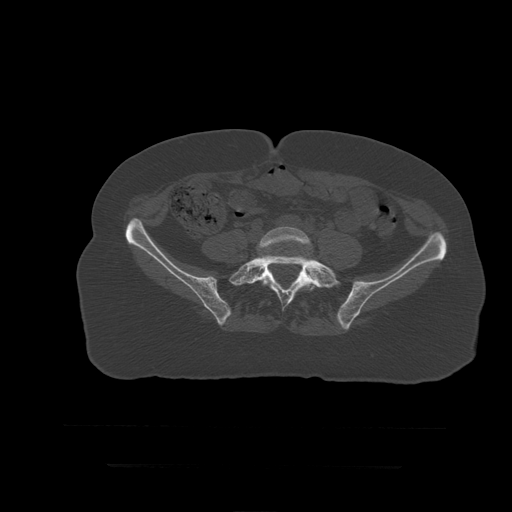
CT including the spine, one axial slice; slice 59 of 399 in the series (ordered by position); bone window (W 1800 / L 400 HU); 1.25 mm slice thickness; 512 × 512 image matrix. Patient age 41 years. From the clinical record (not read from this slice): primary cancer: breast.
Structures marked on this image (semi-automatic segmentation, software-assisted and operator-edited):
- L5 vertebra: box from (x=257, y=227) to (x=316, y=290) px